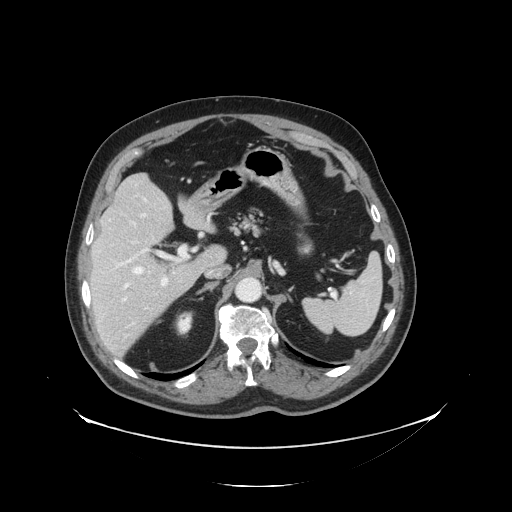
Contrast-enhanced abdominal CT, one axial slice. Position 88 of 138 along the scan axis. 120 kVp. Intravenous contrast given. Soft-tissue window (W 400 / L 40 HU). 2.5 mm slice thickness. 512 × 512 image matrix, field of view 497 × 497 mm. Male patient, age 77 years. Case-level facts recorded for this patient, not image findings: diagnosis: colorectal cancer liver metastases, imaged before liver resection; multiple liver metastases: no; largest metastasis: 1.5 cm; disease in both lobes: no.
Outlined on this slice (manually delineated by an expert):
- hepatic veins: bounding box [x1, y1, x2, y2] px = [124, 214, 145, 287]
- liver: [91, 174, 225, 357]
- planned liver remnant (the part of the liver to remain after resection): [92, 175, 222, 288]
- portal vein (with intrahepatic branches): [116, 246, 188, 302]